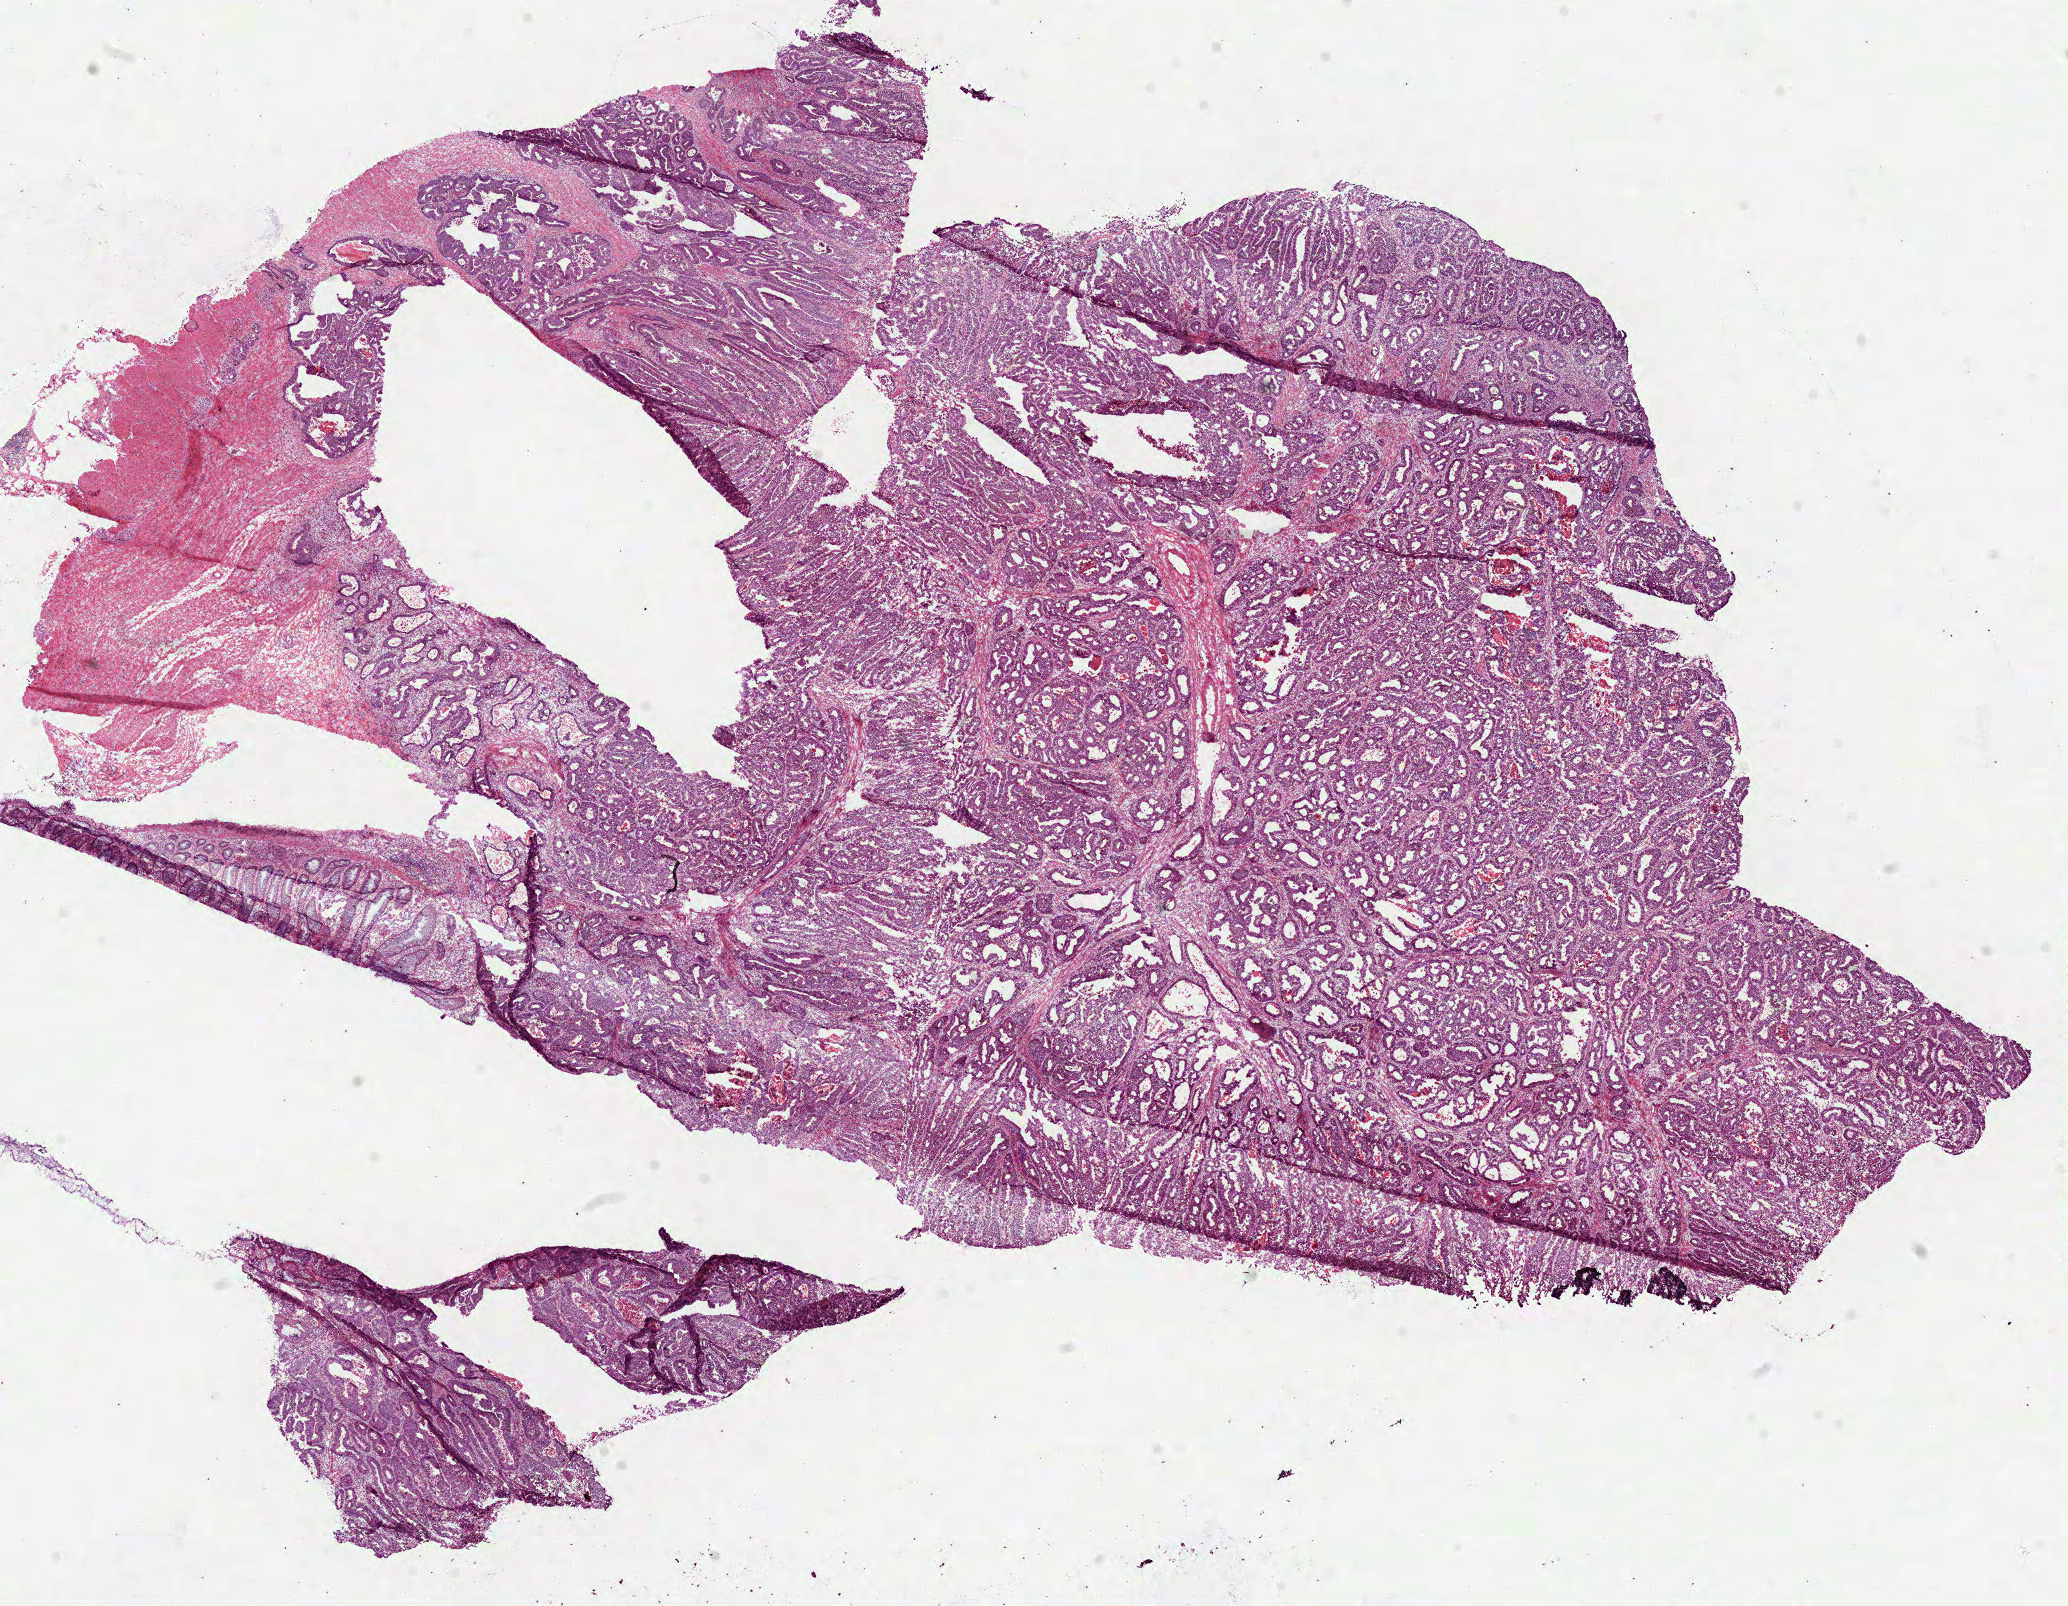
H&E-stained whole-slide image, low-resolution overview of the scanned area, about 16.7 x 13.0 mm (acquisition: 40x scan); frozen section from the bottom of the tissue portion; colon, primary tumour sample. Female patient; age at initial diagnosis 77 years. Pathologist review of this section (percent, as recorded): tumour cells 80%, tumour nuclei 80%, normal cells 5%, stromal cells 10%, necrosis 5%.
* diagnosis: Adenocarcinoma, NOS (sigmoid colon)